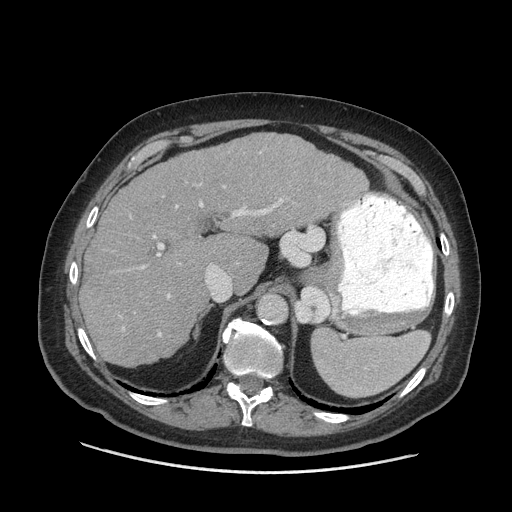
Contrast-enhanced abdominal CT (liver protocol), one axial slice; slice 46 of 77 in the series (ordered by position); reconstruction kernel STANDARD; soft-tissue window (W 400 / L 40 HU); 2.5 mm slice thickness; 512 × 512 image matrix, field of view 420 × 420 mm. From the clinical record (not read from this slice): diagnosis: hepatocellular carcinoma (patient treated with transarterial chemoembolisation; whether this scan precedes or follows treatment is not stated here); TNM stage (as recorded): Stage-I; Child-Pugh class: A; tumour differentiation: well differentiated; tumour nodularity: uninodular.
Outlined on this slice (semi-automatic segmentation, software-assisted and operator-edited):
- liver parenchyma outside the tumour (the mass and vessels are separate outlines, so this box may not span the whole liver): bounding box (x1, y1, x2, y2) in pixels: (80, 134, 368, 366)
- liver vessels: (122, 186, 283, 336)